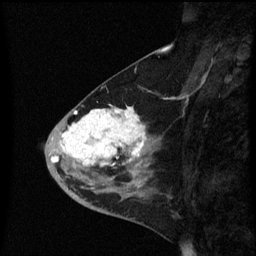
Breast MRI (dynamic contrast-enhanced), one sagittal slice; slice 25 of 60 in the series (ordered by position); dynamic contrast-enhanced series, image 2 of 3 at this slice position (ordered by acquisition); 1.5 T; TE 4.2 ms, TR 8.4 ms; 256 × 256 image matrix, field of view 200 × 200 mm. Female patient, age 46 years. From the clinical record (not read from this slice): setting: breast cancer imaged before/during neoadjuvant chemotherapy; receptor status: HER2-positive.
Structures marked on this image (semi-automatically segmented with operator editing):
- analysis volume of interest (the breast-tissue region the enhancement analysis was run in; not a lesion): bounding box (x1, y1, x2, y2) in pixels: (45, 96, 161, 187)
- tumour enhancement mask (voxels above the 70 % enhancement threshold inside the analysis volume of interest): (51, 106, 147, 183)